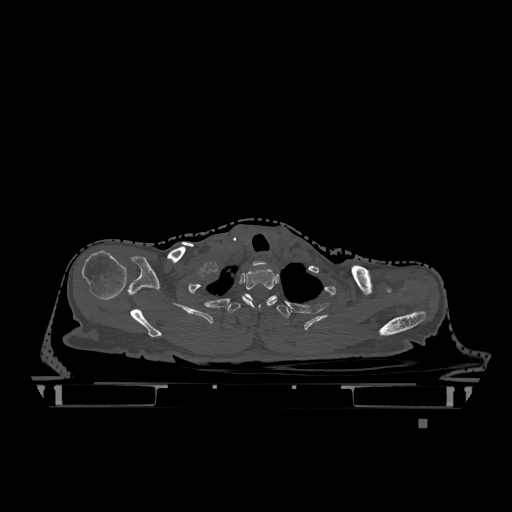
CT including the spine, one axial slice; slice 987 of 1317 in the series (ordered by position); bone window (W 1800 / L 400 HU); 512 × 512 image matrix, field of view 500 × 500 mm. Female patient, age 74 years. From the clinical record (not read from this slice): primary cancer: lung; vertebrae with lytic lesions (as recorded): T1, T4, T5, T6, L4, L5.
Outlined on this slice (semi-automatic segmentation, software-assisted and operator-edited):
- T1 vertebra: box from (x=241, y=268) to (x=277, y=308) px
- T2 vertebra: (x=228, y=294)–(x=291, y=318)